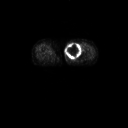
FDG PET of an extremity soft-tissue mass (from a PET/CT study), one axial slice. Position 30 of 91 along the scan axis. 128 × 128 image matrix. Female patient, age 74 years. Case-level facts recorded for this patient, not image findings: histological type: pleomorphic leiomyosarcoma; grade: high; site of the primary tumour: left thigh.
Structures marked on this image (expert contour drawn on MRI and transferred to this co-registered scan by the dataset authors):
- gross tumour volume including surrounding oedema: box from (x=65, y=42) to (x=82, y=59) px
- gross tumour volume (mass): (x=65, y=42)–(x=82, y=59)